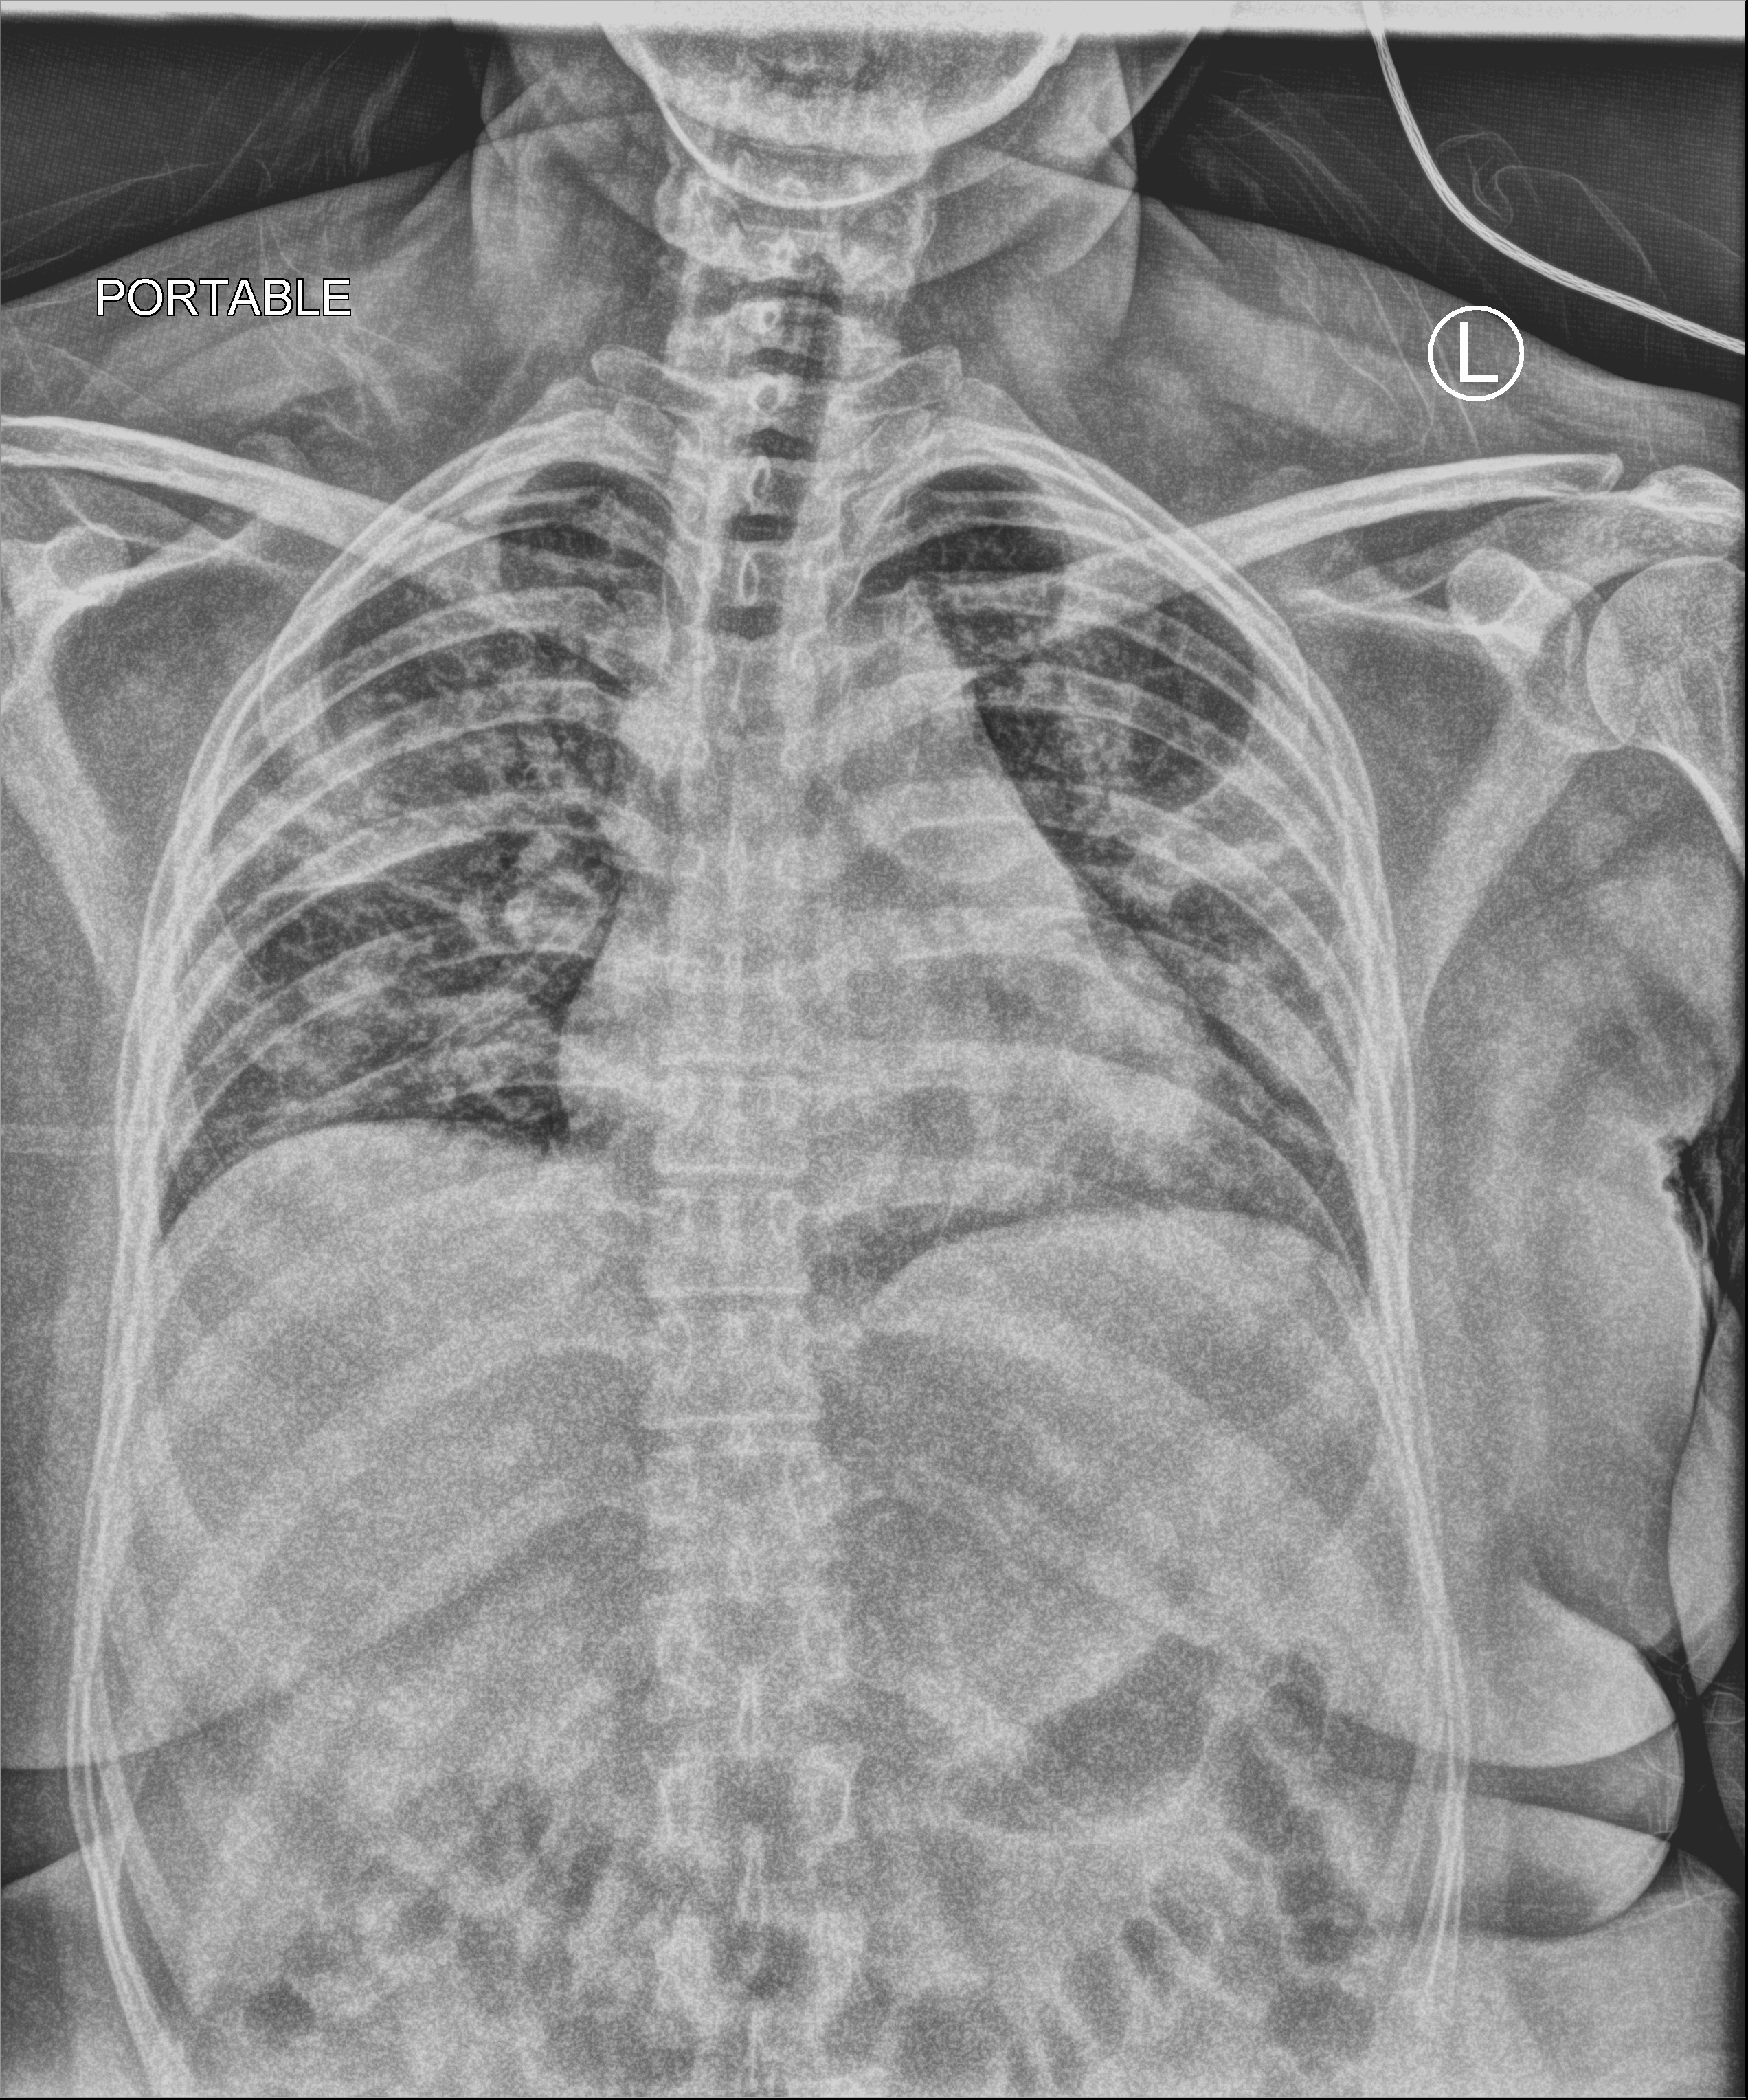
Bedside chest radiograph (computed radiography), anteroposterior (AP) projection. Patient hospitalised with COVID-19; female, aged 18–59 years.
From the hospital-stay record, not from the radiograph (when in the stay this image was taken is not recorded): admitted to intensive care during this hospital stay: no.